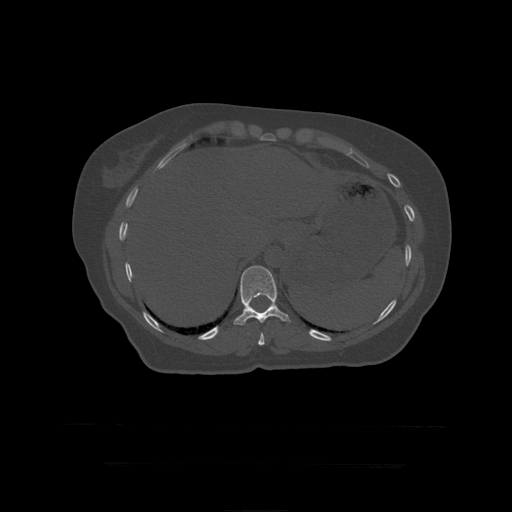
CT including the spine, one axial slice. Slice 222 of 399 in the series (ordered by position). Reconstruction kernel STANDARD. Bone window (W 1800 / L 400 HU). 1.25 mm slice thickness. 512 × 512 image matrix. Patient age 41 years. Case-level facts recorded for this patient, not image findings: primary cancer: breast.
Structures marked on this image (semi-automatic segmentation, software-assisted and operator-edited):
- T10 vertebra: bounding box <258,332,265,346> (left, top, right, bottom; pixels)
- T11 vertebra: <234,266,291,326>